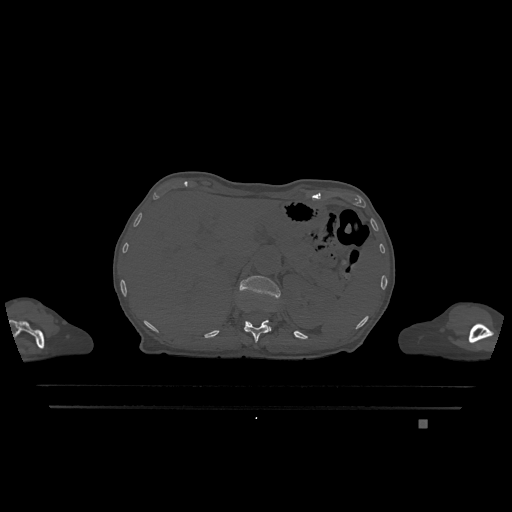
CT including the spine, one axial slice; bone window (W 1800 / L 400 HU); 0.5 mm slice thickness; 512 × 512 image matrix, field of view 500 × 500 mm. Patient: female, 74 years. Case-level facts recorded for this patient, not image findings: primary cancer: lung; vertebrae with lytic lesions (as recorded): T1, T4, T5, T6, L4, L5.
Outlined on this slice (semi-automatic segmentation, software-assisted and operator-edited):
- L1 vertebra: bounding box <239,276,280,331> (left, top, right, bottom; pixels)
- T12 vertebra: <244,320,270,342>